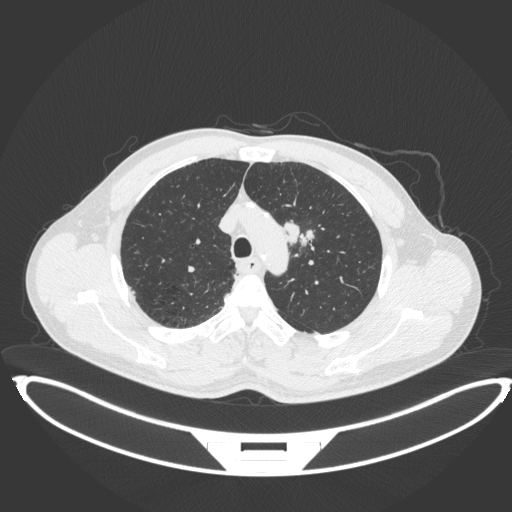
Chest CT, one axial slice; slice 332 of 407 in the series (ordered by position); reconstruction kernel B31f; lung window (W 1500 / L -600 HU); 1 mm slice thickness; 512 × 512 image matrix, field of view 457 × 457 mm. Male patient, age 60 years. From the clinical record (not read from this slice): clinical TNM (as recorded): T2a N0 M0.
Structures marked on this image (bounding box drawn by a radiologist):
- lung tumour (recorded histology: squamous cell carcinoma): bounding box (x1, y1, x2, y2) in pixels: (282, 218, 318, 249)